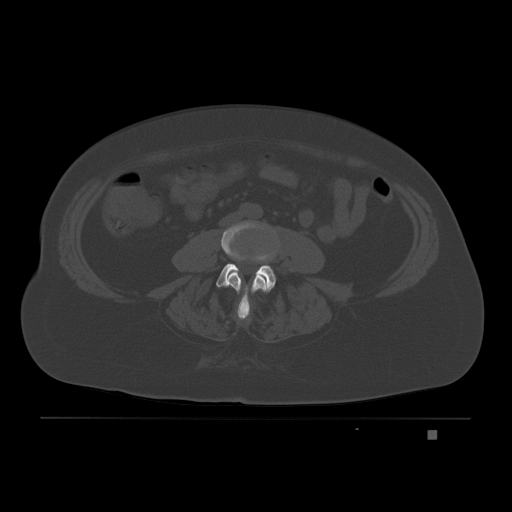
CT including the spine, one axial slice. Slice 45 of 221 in the series (ordered by position). Bone window (W 1800 / L 400 HU). 3 mm slice thickness. 512 × 512 image matrix, field of view 474 × 474 mm. Female patient, age 63 years. From the clinical record (not read from this slice): primary cancer: breast.
Structures marked on this image (semi-automatically segmented with operator editing):
- L3 vertebra: box from (x=221, y=221) to (x=274, y=318) px
- L4 vertebra: (x=216, y=263)–(x=276, y=321)